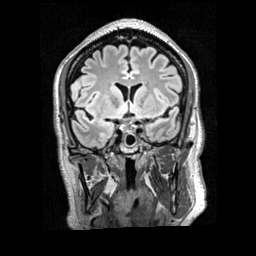
Brain MRI from a brain-tumour surgery series, one coronal slice. Position 122 of 200 along the scan axis. T2 FLAIR. 1 mm slice thickness. 256 × 256 image matrix, field of view 256 × 256 mm. From the clinical record (not read from this slice): histopathology: Glioblastoma; WHO grade: 4; IDH mutation: no; tumour location: Right Frontal.
Outlined on this slice (manually delineated by an expert):
- tumour: bounding box <70,74,94,87> (left, top, right, bottom; pixels)